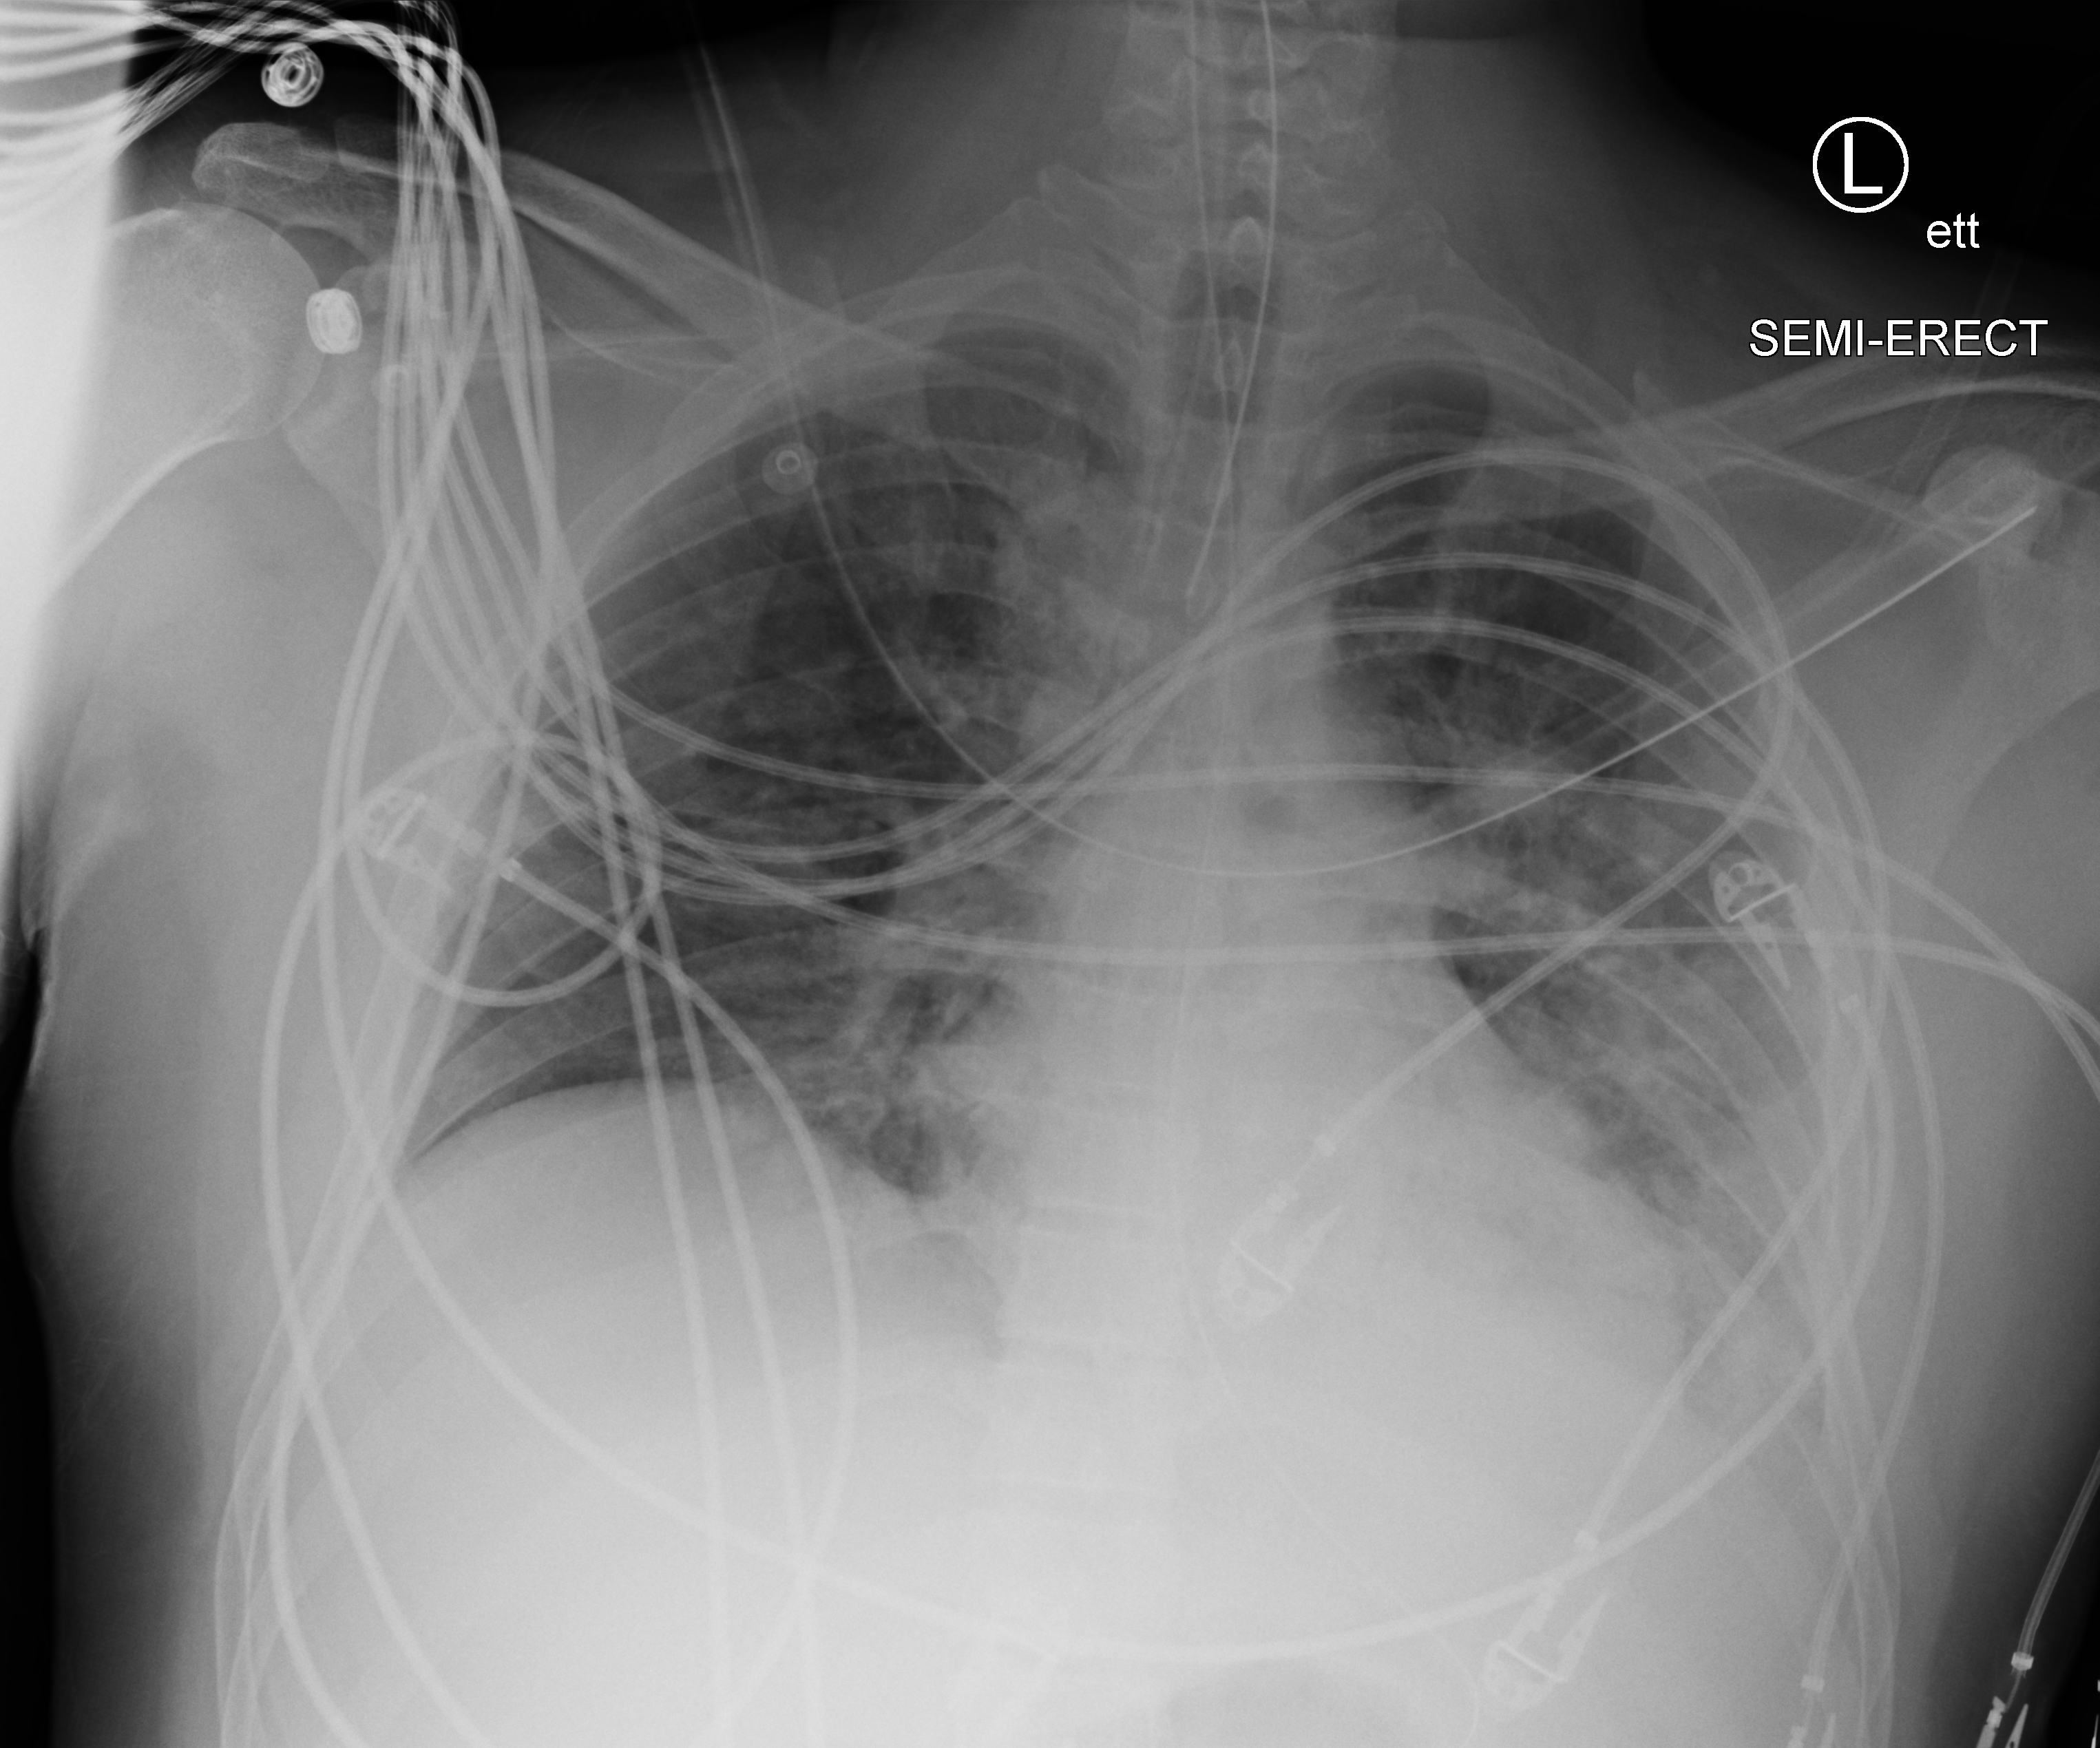
Bedside chest radiograph (computed radiography), anteroposterior (AP) projection. Patient hospitalised with COVID-19, aged 18–59 years.
Admission-level facts for this patient (not findings on this image; timing relative to this image not recorded): chronic kidney disease (admission record): no.